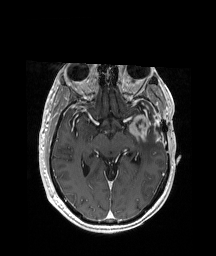
Brain MRI from a brain-tumour surgery series, one axial slice. Slice 118 of 208 in the series (ordered by position). T1-weighted post-contrast. 1 mm slice thickness. 216 × 256 image matrix, field of view 228 × 270 mm. From the clinical record (not read from this slice): histopathology: Glioblastoma; WHO grade: 4; IDH mutation: no; tumour location: Left Anterior/Superior Temporal.
Annotated regions visible in this slice (expert manual segmentation):
- previous resection cavity: bounding box [x1, y1, x2, y2] px = [137, 120, 141, 127]
- tumour: [123, 112, 158, 140]